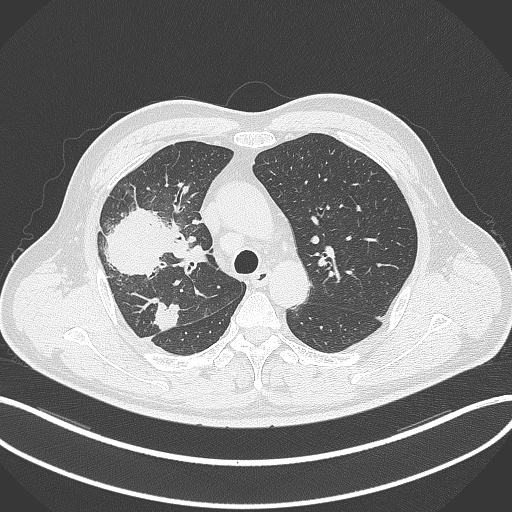
Chest CT, one axial slice; slice 231 of 348 in the series (ordered by position); reconstruction kernel B70f; lung window (W 1500 / L -600 HU); 512 × 512 image matrix, field of view 400 × 400 mm. Patient: male, 55 years. Case-level facts recorded for this patient, not image findings: clinical TNM (as recorded): T3 N2 M1.
Outlined on this slice (rectangle marked by the reading radiologist):
- lung tumour (recorded histology: adenocarcinoma): bounding box (x1, y1, x2, y2) in pixels: (99, 209, 179, 277)